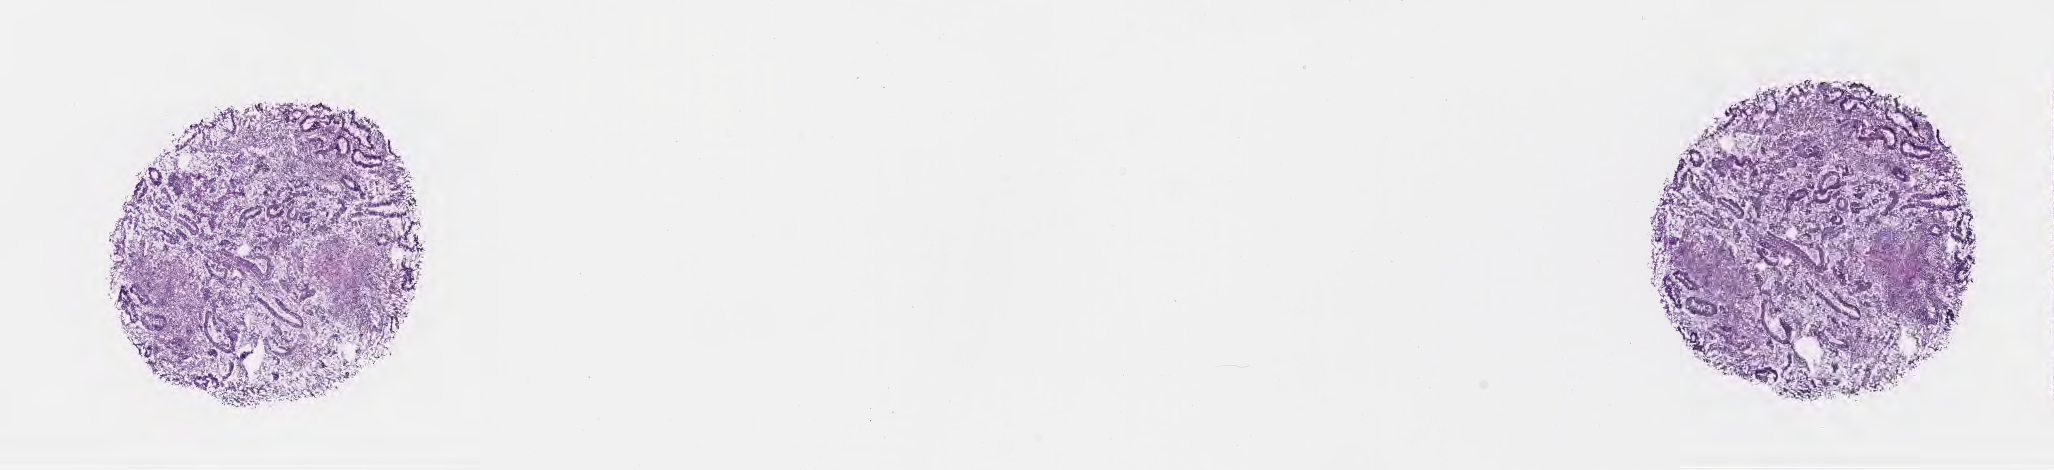
Digitized H&E-stained section — shown as a low-resolution overview of the whole scanned area (about 16.6 x 3.8 mm). Frozen section (tissue freezing medium). Specimen: primary tumor. Site: sigmoid colon. Patient: male, age at initial diagnosis 67 years. Tumor grade: G2 (moderately differentiated). Composition of this section per pathologist review: tumor cells 65%, tumor nuclei 65%, stromal cells 25%, necrosis 0%, normal cells 10%. Inflammatory infiltration, as recorded: lymphocyte infiltration 7%, monocyte infiltration 3%, neutrophil infiltration 8%.
AJCC pathologic stage: Stage IIIC. Histologic diagnosis: Adenocarcinoma, NOS.